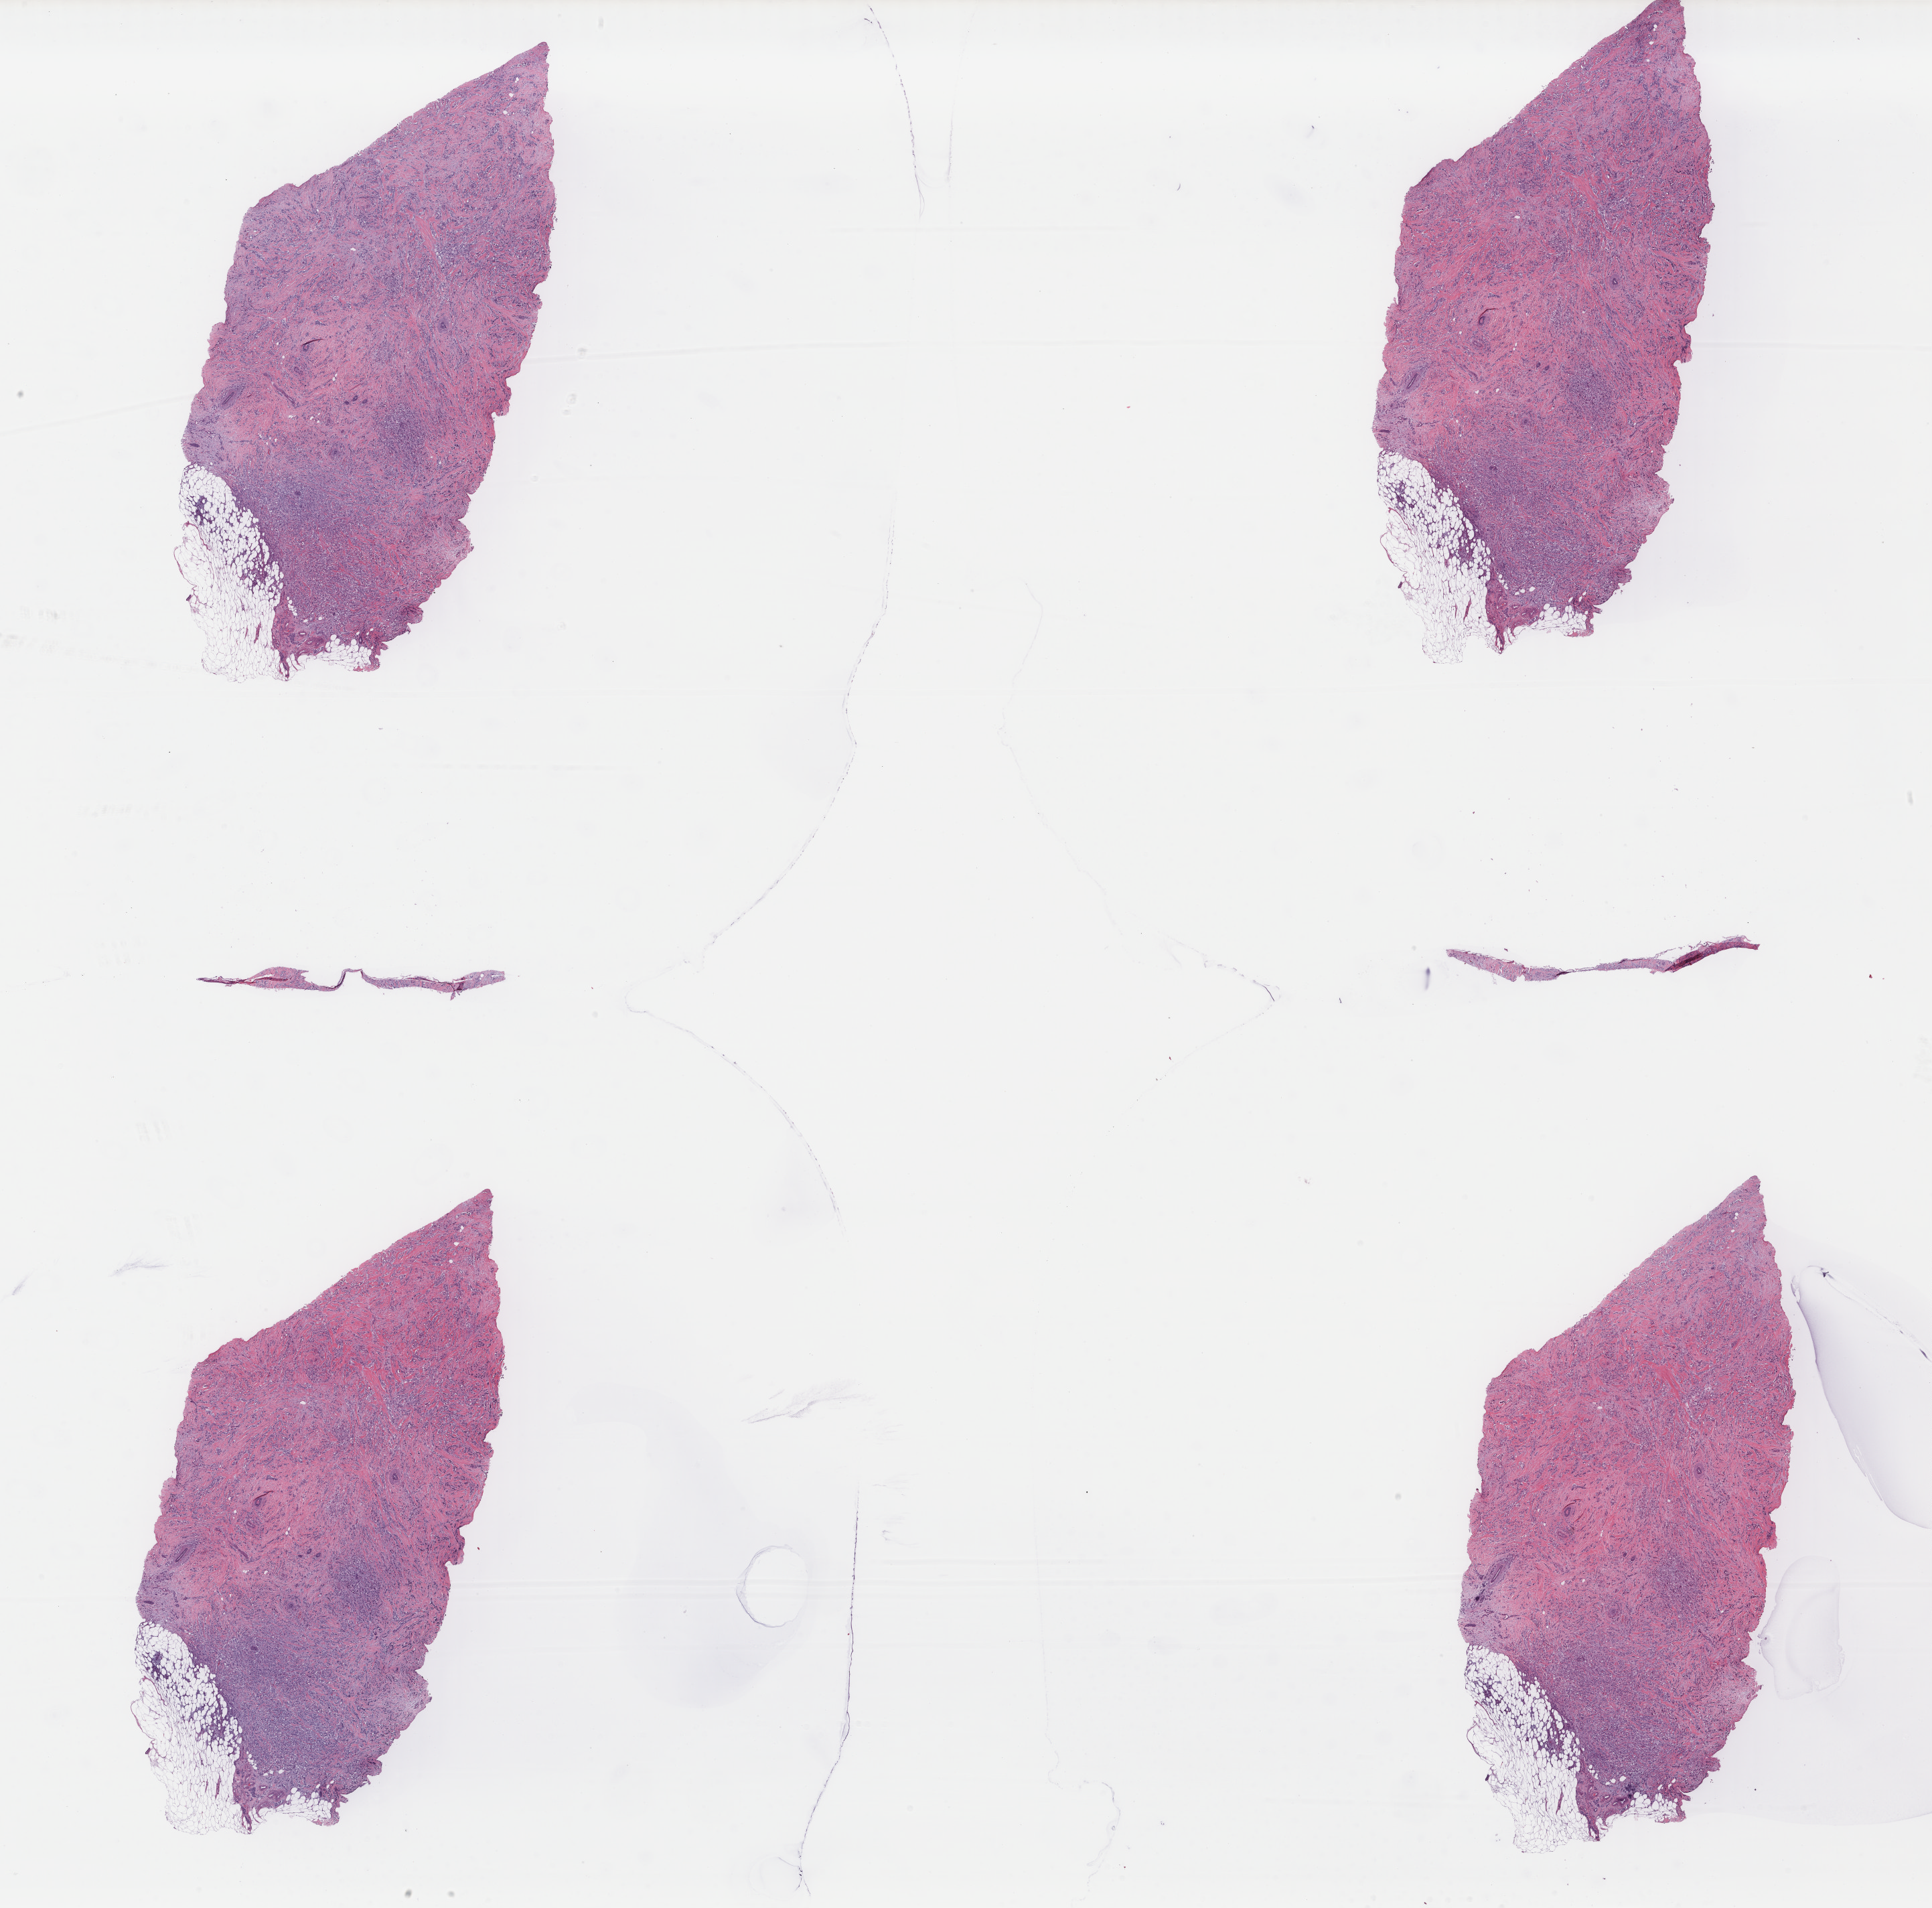
H&E-stained whole-slide image, whole scanned area (about 22.9 x 22.6 mm, acquisition: 40x scan) shown as a low-resolution overview; formalin-fixed paraffin-embedded (FFPE) diagnostic section; primary tumour sample from the breast. Female patient; age at initial diagnosis 71 years.
- lymph nodes positive (case pathology): 0 of 16 examined
- AJCC pathologic stage: IIIA (7th edition)
- histologic diagnosis: Lobular carcinoma, NOS